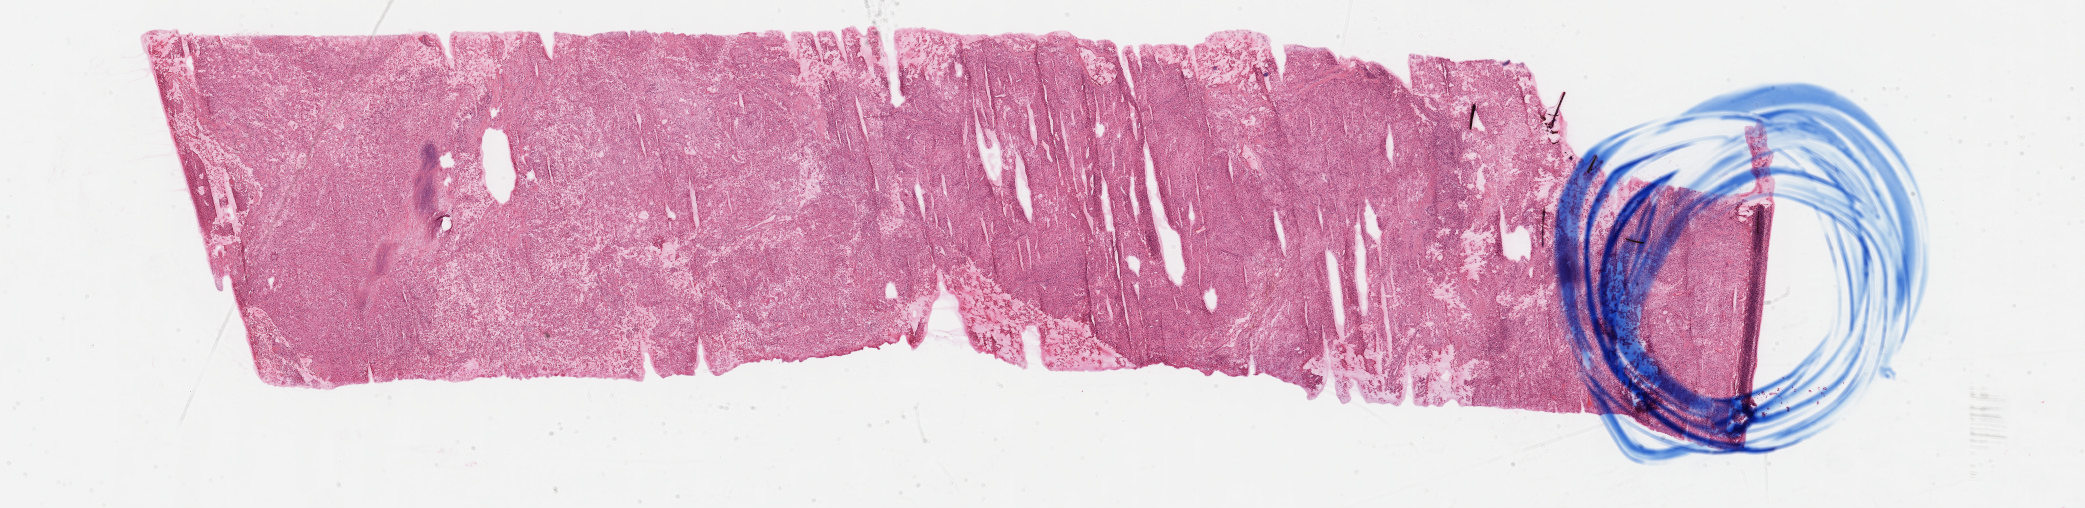
H&E-stained whole-slide image, low-resolution overview of the scanned area, about 33.7 x 8.2 mm (from a 40x scan); FFPE section; kidney, primary tumour sample. Patient: male, age at initial diagnosis 73 years. Histologic grade: G4 (undifferentiated).
- histologic diagnosis: Clear cell adenocarcinoma, NOS
- AJCC pathologic stage: III